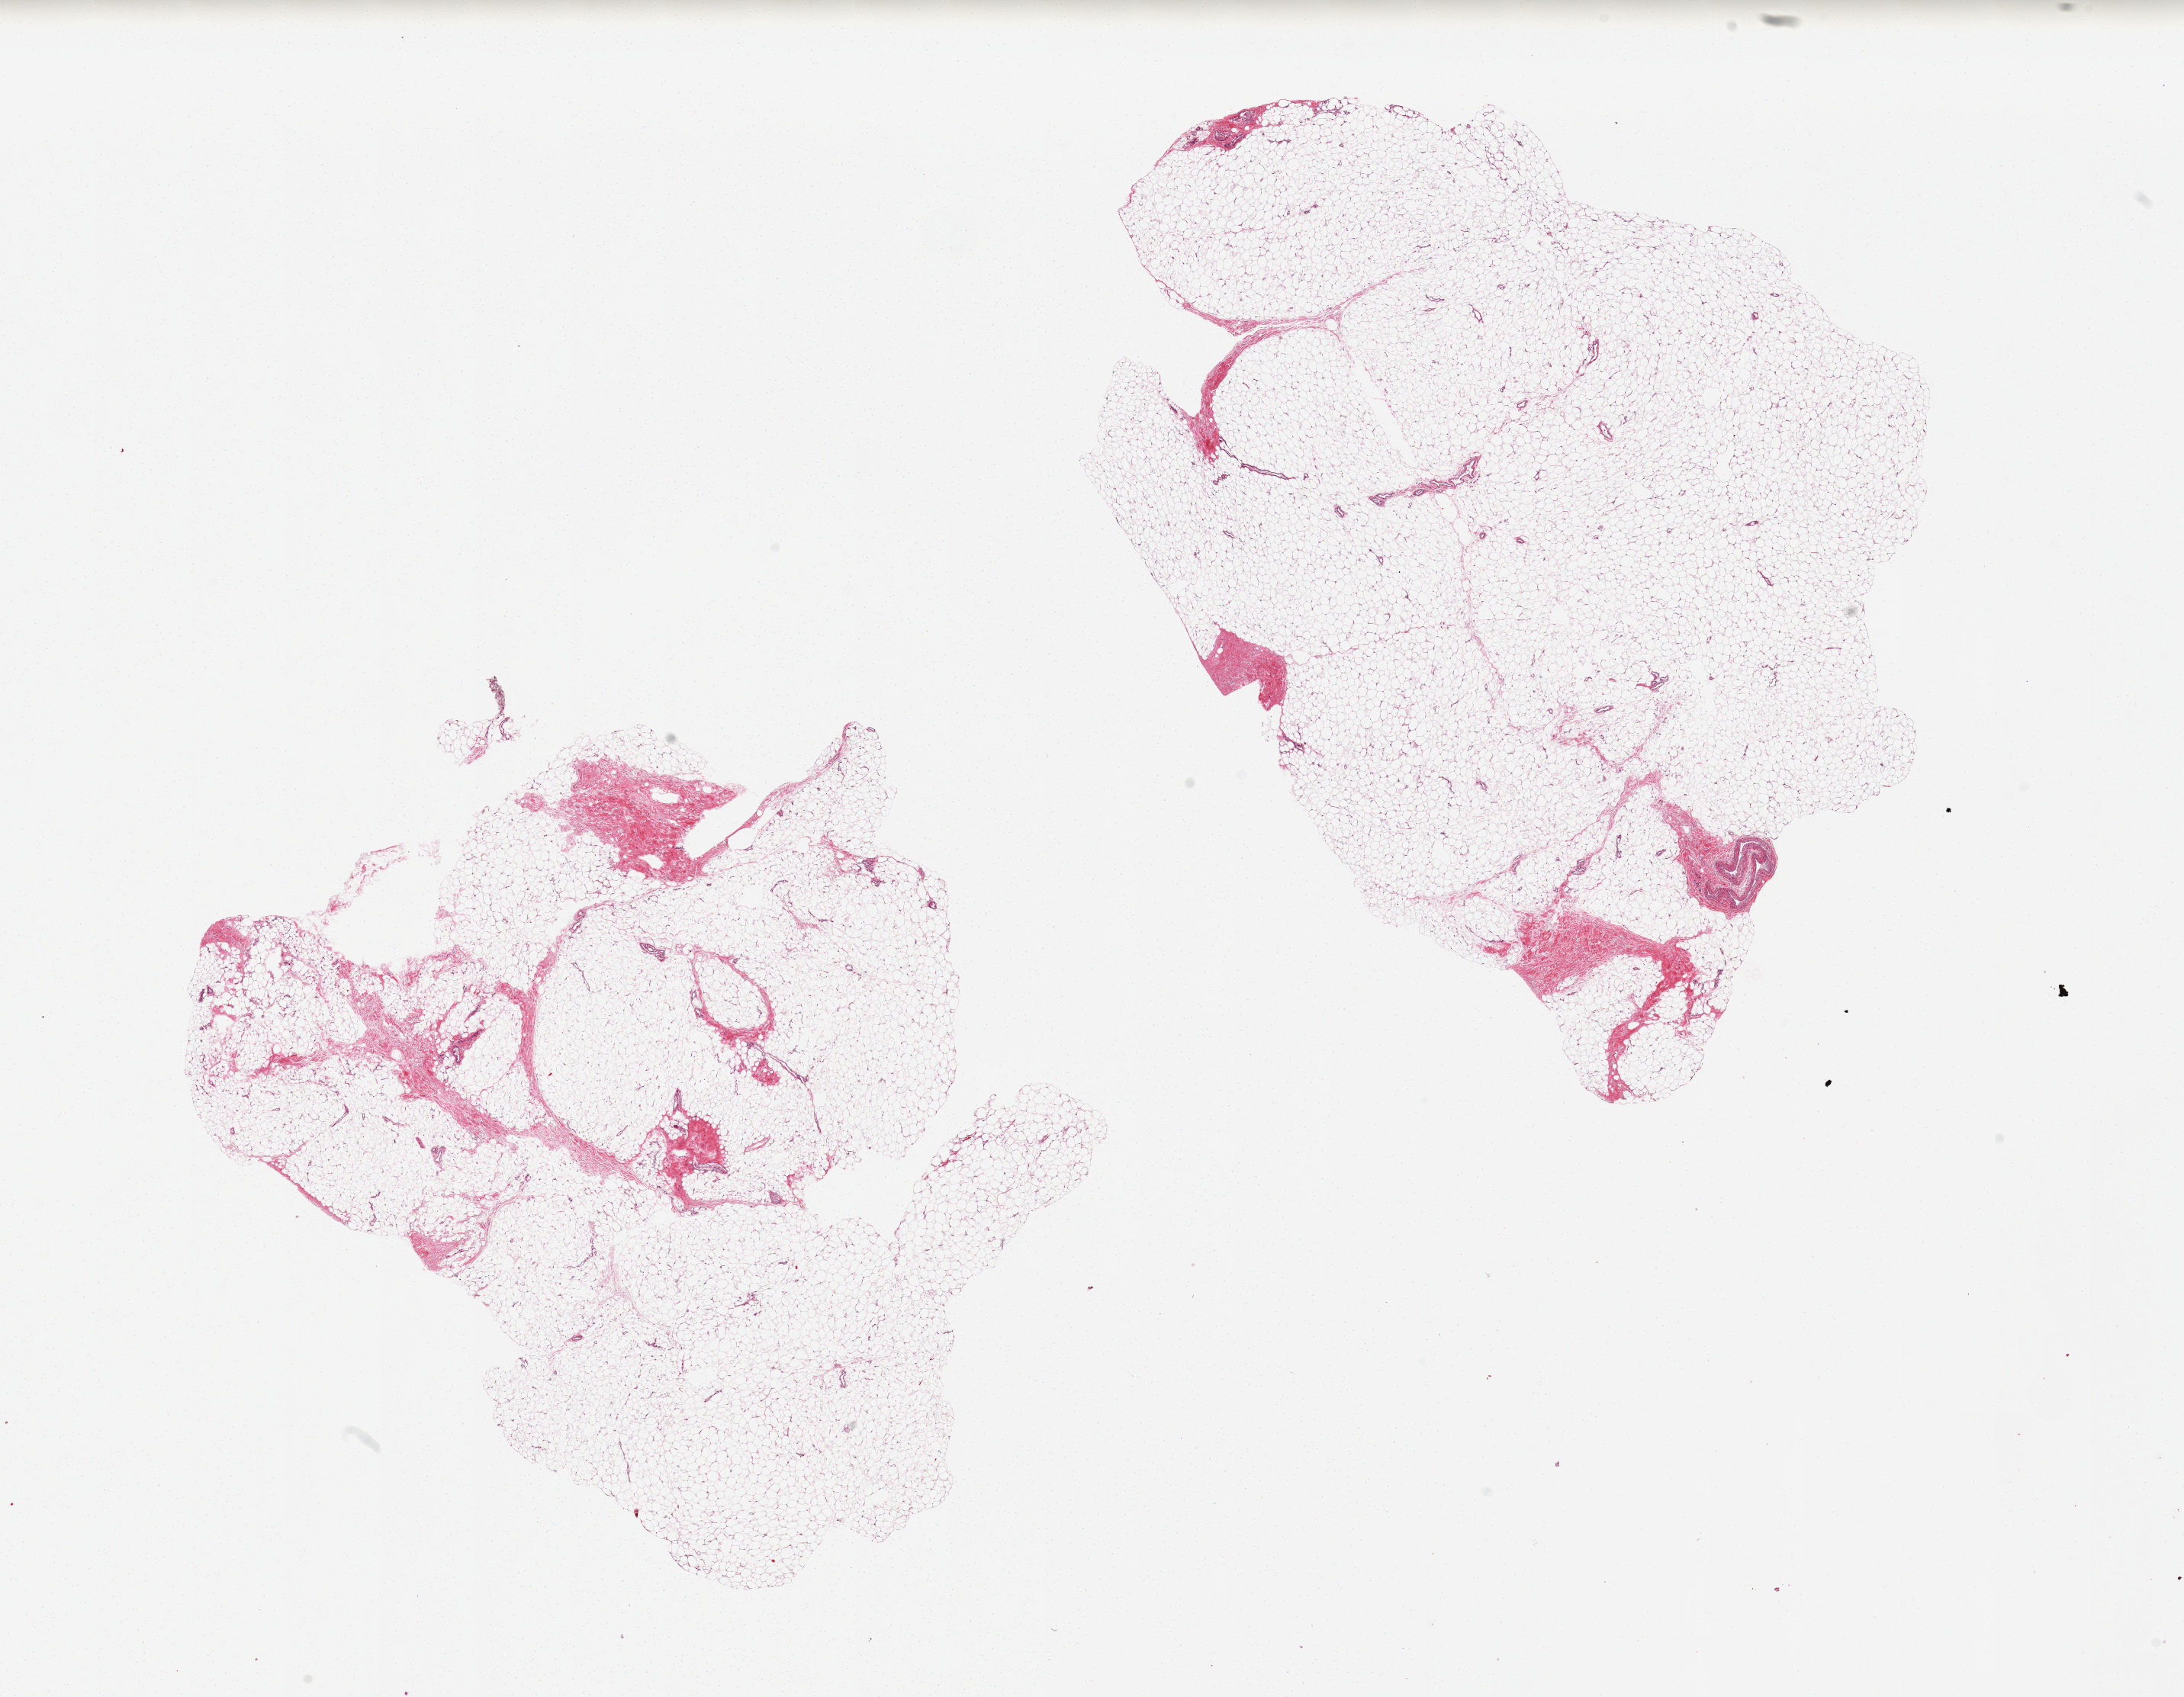
Digitized H&E-stained section — whole scanned area (about 22.6 x 17.6 mm) shown as a low-resolution overview; PAXgene-fixed paraffin-embedded (PFPE) section; section of adipose tissue (target tissue); donor tissue sample.
Pathologist's review note for this sample: 2 pieces, ~5% fibrous tissue.